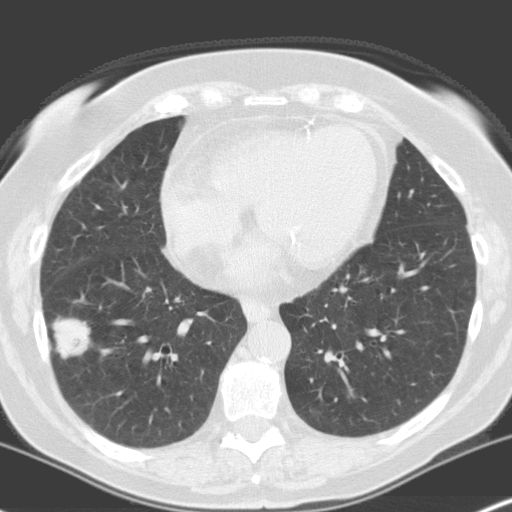
Axial slice from a low-dose chest CT screening exam; first (baseline) screen; lung window (W 1500 / L -600 HU); 3.2 mm slice thickness; 512 × 512 image matrix. Female, age 70 years at enrolment. Current smoker at enrolment.
- Expert reader's lesion annotation, bounding box (x1, y1, x2, y2) in pixels: (34, 305, 101, 374).
- The screening reader recorded 4 non-calcified nodules or masses ≥4 mm on this exam (right lower lobe, right upper lobe, left upper lobe, left upper lobe); which of them this box marks is not recorded.
- Participant outcome: lung cancer diagnosed 28 days after this screen — adenocarcinoma, NOS, right lower lobe, moderately differentiated (G2), stage IV (AJCC 6th edition), 28 mm at pathology.